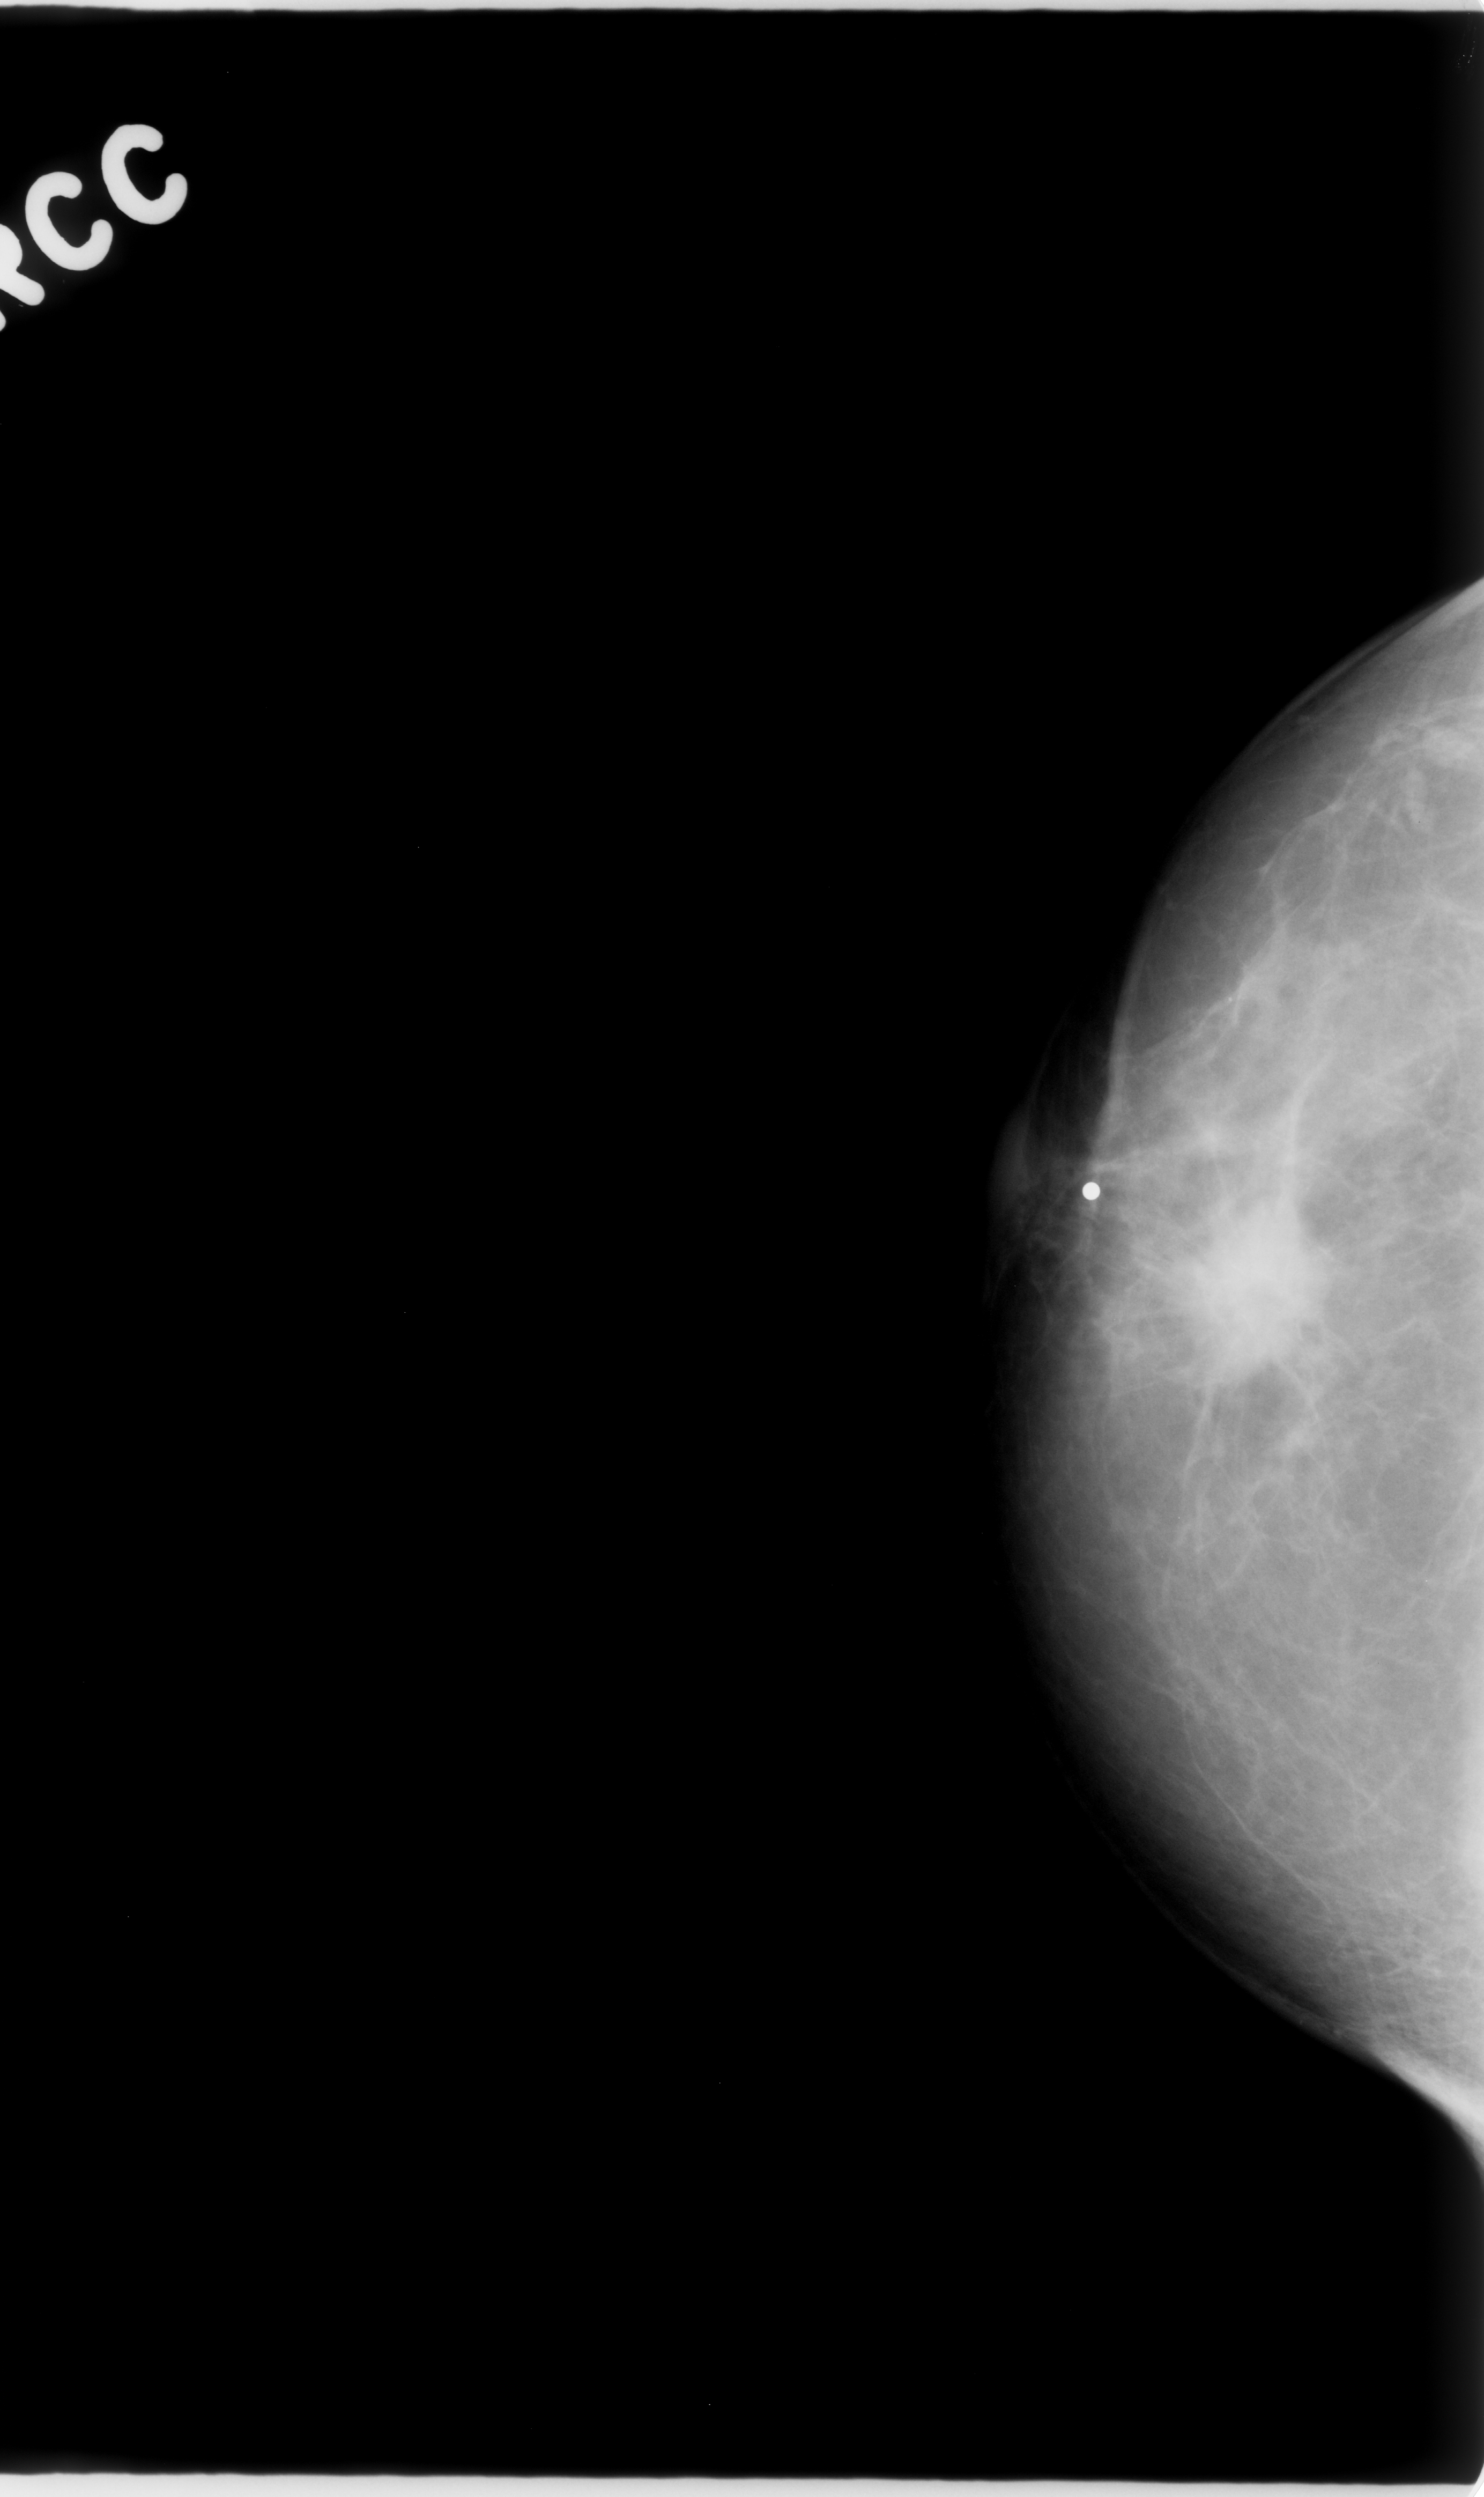
Mammogram (digitized film); right breast; CC view; BI-RADS breast density category 1 (scale 1–4).
Radiologist-marked abnormalities on this image: mass, shape irregular, margins spiculated; BI-RADS assessment category 5; pathology result (as recorded, not read from the image): malignant.